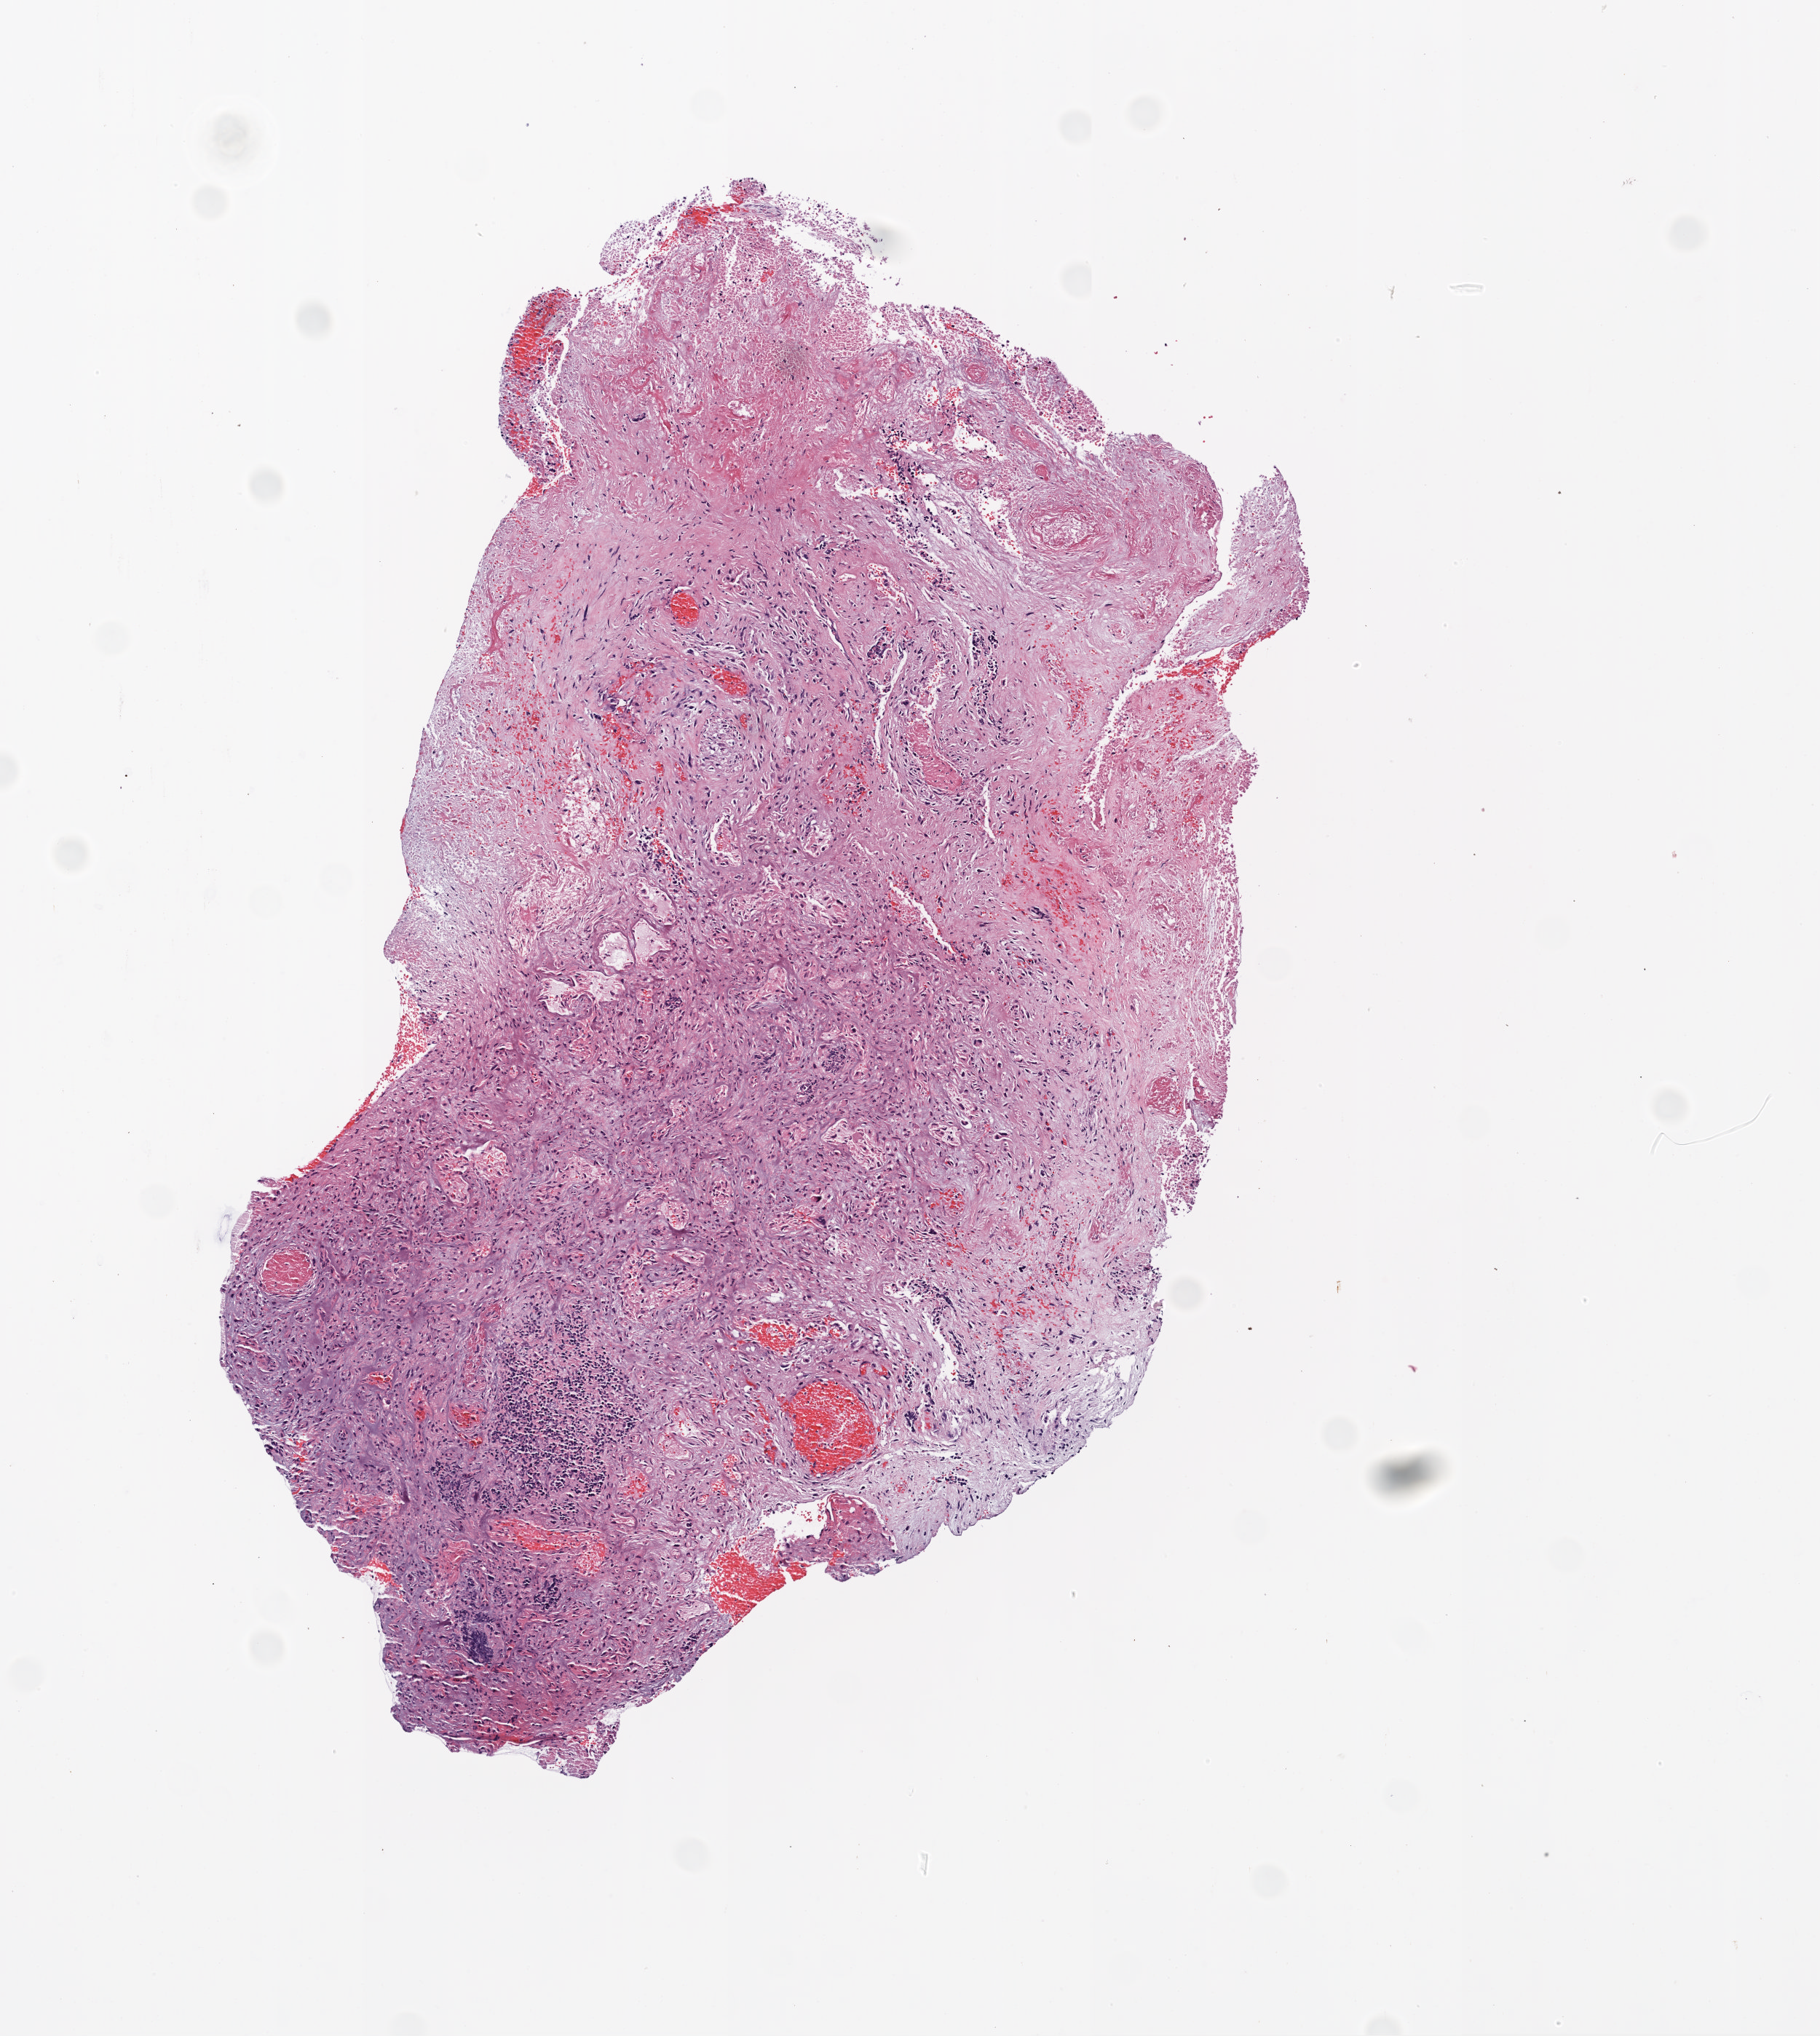
H&E-stained whole-slide image — shown as a low-resolution overview of the whole scanned area (about 5.0 x 5.6 mm, acquisition: 20x scan), FFPE section, primary tumour sample from the brain. Patient: male, age at initial diagnosis 75 years.
Pathologic diagnosis: Glioblastoma.